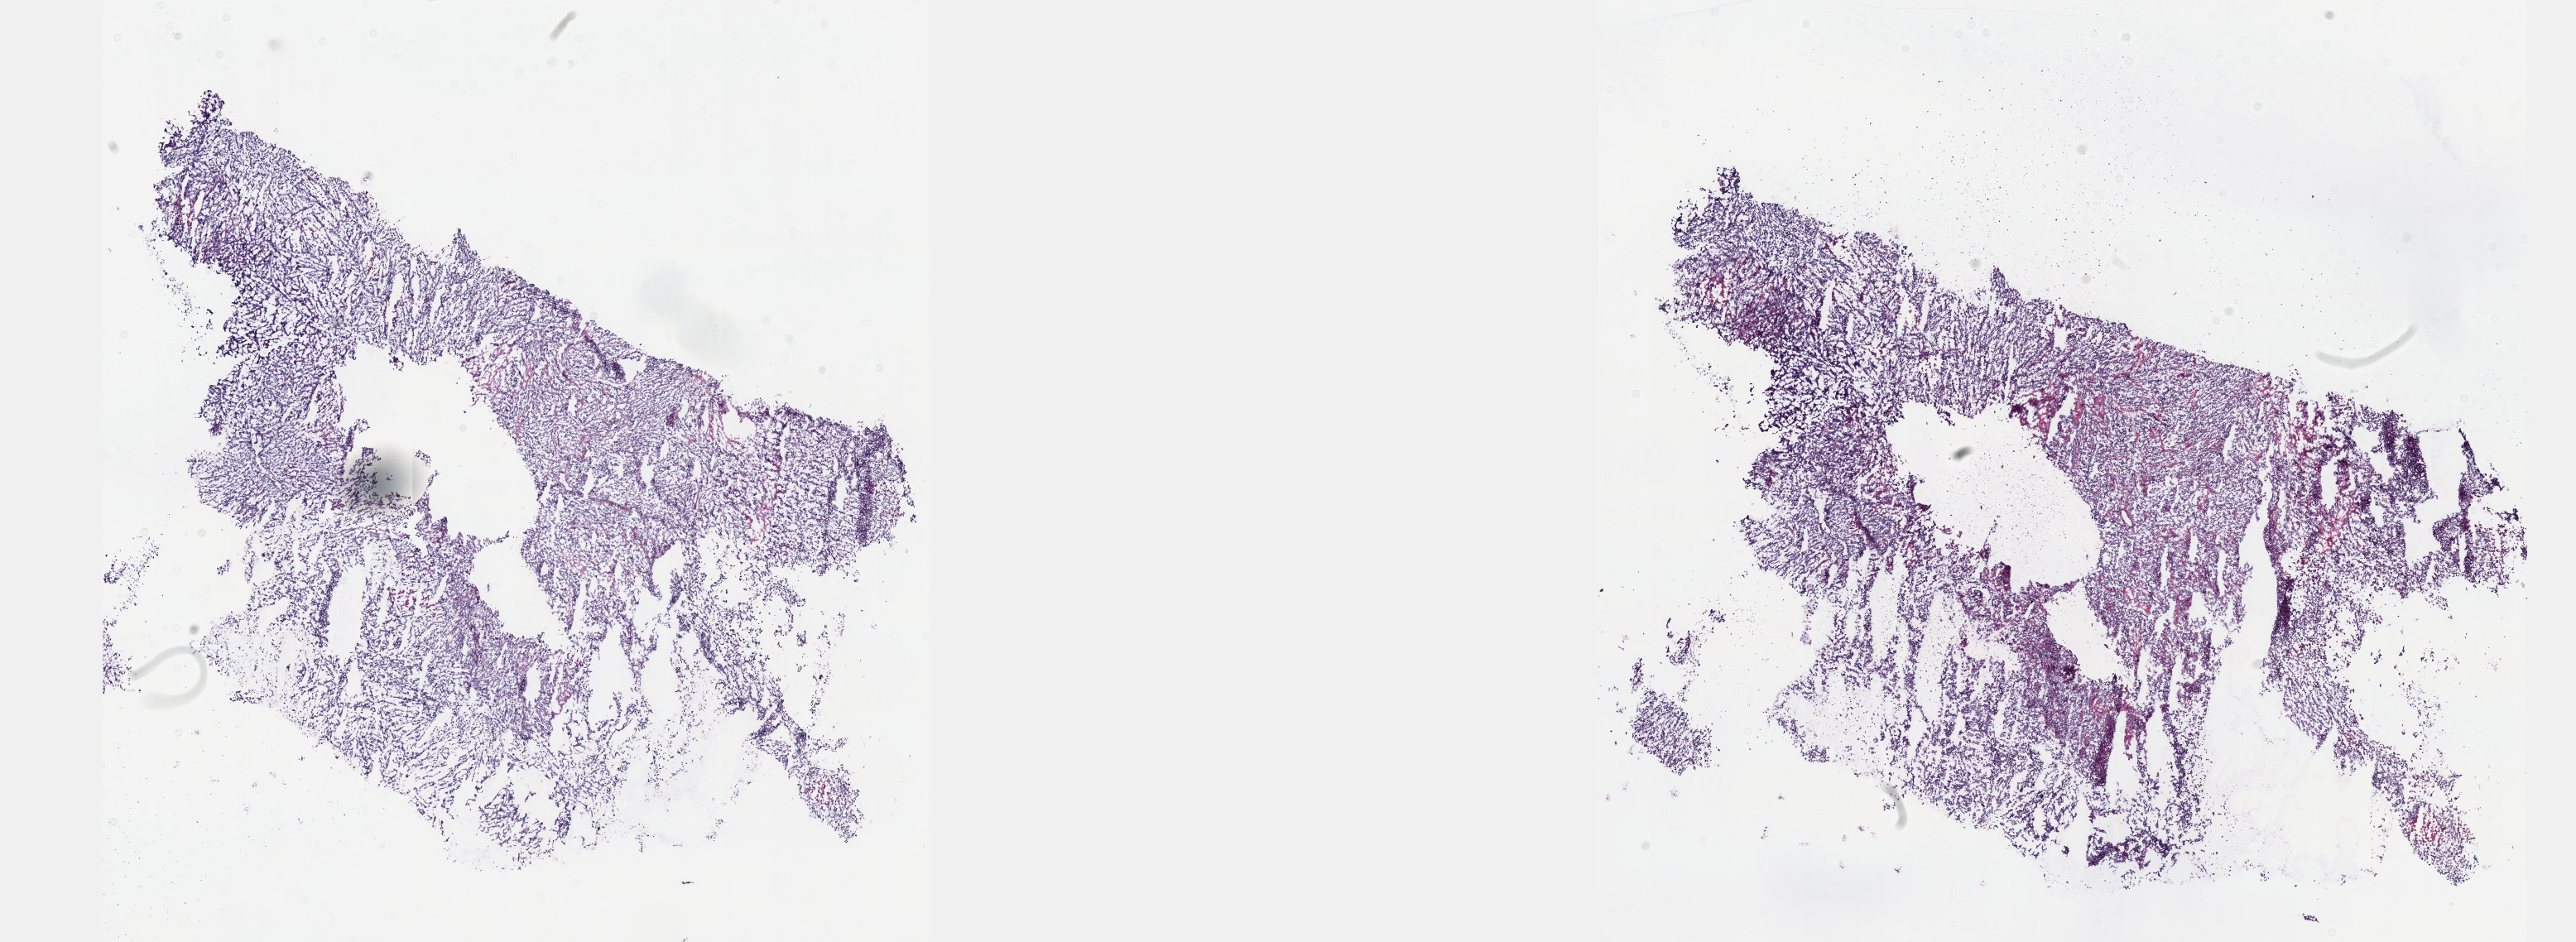
H&E whole-slide image, low-resolution overview of the scanned area, about 25.1 x 9.2 mm (from a 40x scan). Frozen section from the top of the tissue portion. Testis, primary tumour sample. Male patient; age at initial diagnosis 34 years. Pathologist review of this section (percent, as recorded): tumour cells 100%, tumour nuclei 65%, normal cells 0%, stromal cells 0%, necrosis 0%. Infiltration values recorded for this section: lymphocyte infiltration 0%, monocyte infiltration 0%, neutrophil infiltration 0%.
AJCC pathologic stage: IIIC. Diagnosis: Seminoma, NOS. Laterality: left.